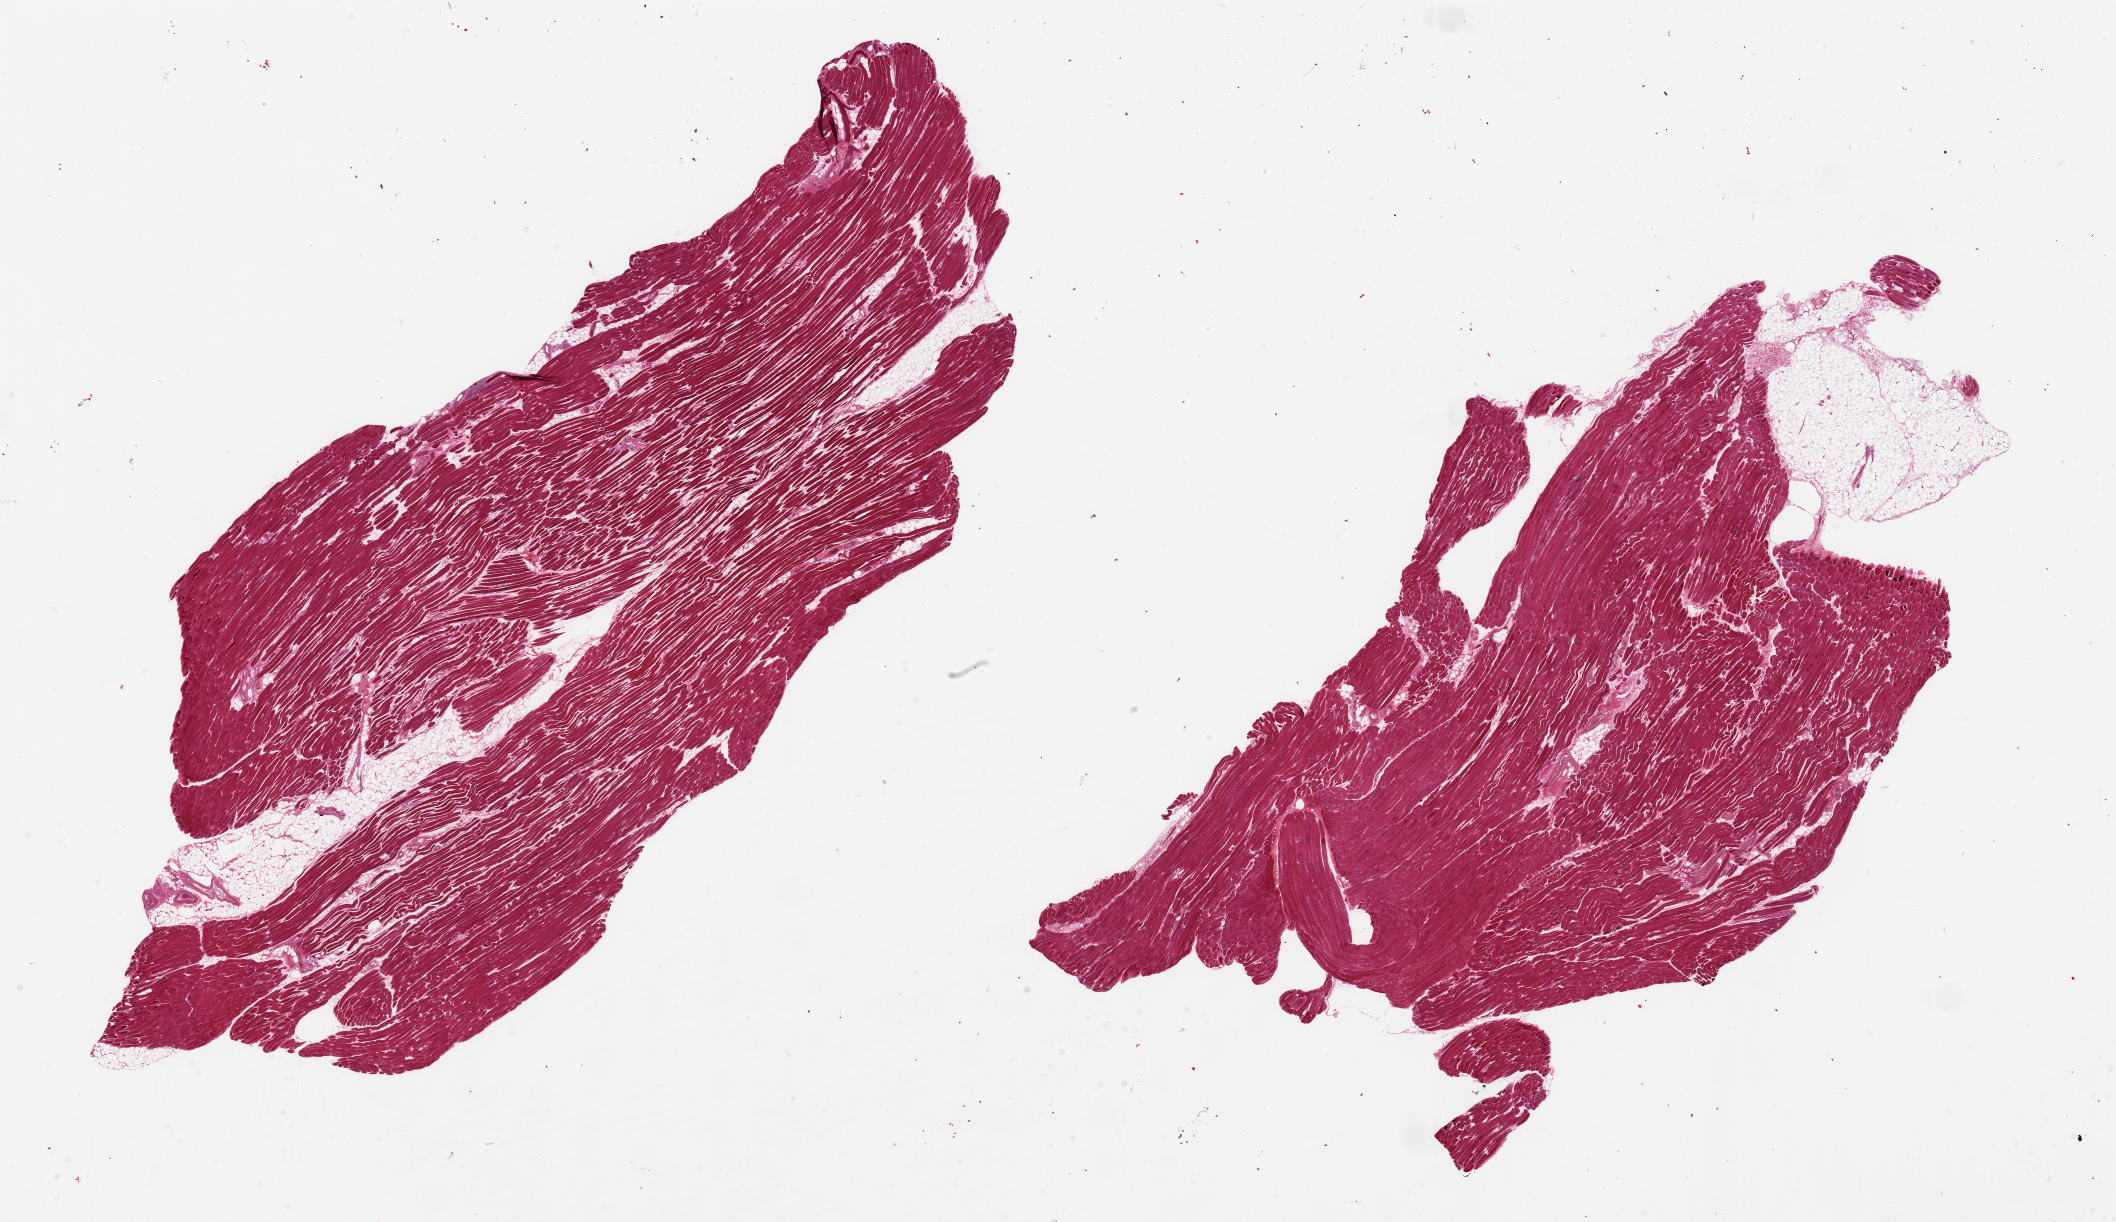
Whole-slide image, hematoxylin and eosin (H&E) stain — whole scanned area (about 33.5 x 19.3 mm) shown as a low-resolution overview; PAXgene-fixed paraffin-embedded (PFPE) section; section of skeletal muscle (target tissue); donor tissue sample. Donor sex: male.
Reviewer comment on this tissue sample: 2 pieces; 1 with 10% peripheral fat.